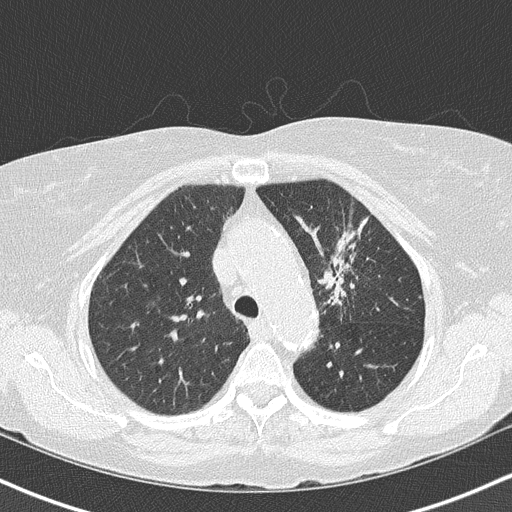
Axial slice from a low-dose chest CT screening exam, third annual screen, lung window (W 1500 / L -600 HU), 2 mm slice thickness, lung (sharp) reconstruction kernel (B50f), 120 kVp, slice 109 of 147 in the series. Female, age 68 years at enrolment. Former smoker at enrolment.
Expert-annotated lung lesion, bounding box <303,205,384,315> (left, top, right, bottom; pixels). Reader record for this screening exam (exam-level; its link to the box is not recorded): non-calcified nodule or mass ≥4 mm, left upper lobe, 5 × 5 mm, poorly defined margins, mixed attenuation, pre-existing on the prior screen: yes; interval growth: yes. Later outcome: lung cancer diagnosed 42 days after this screen — adenocarcinoma, NOS, left upper lobe, poorly differentiated (G3), stage IB (AJCC 6th edition), 50 mm at pathology.